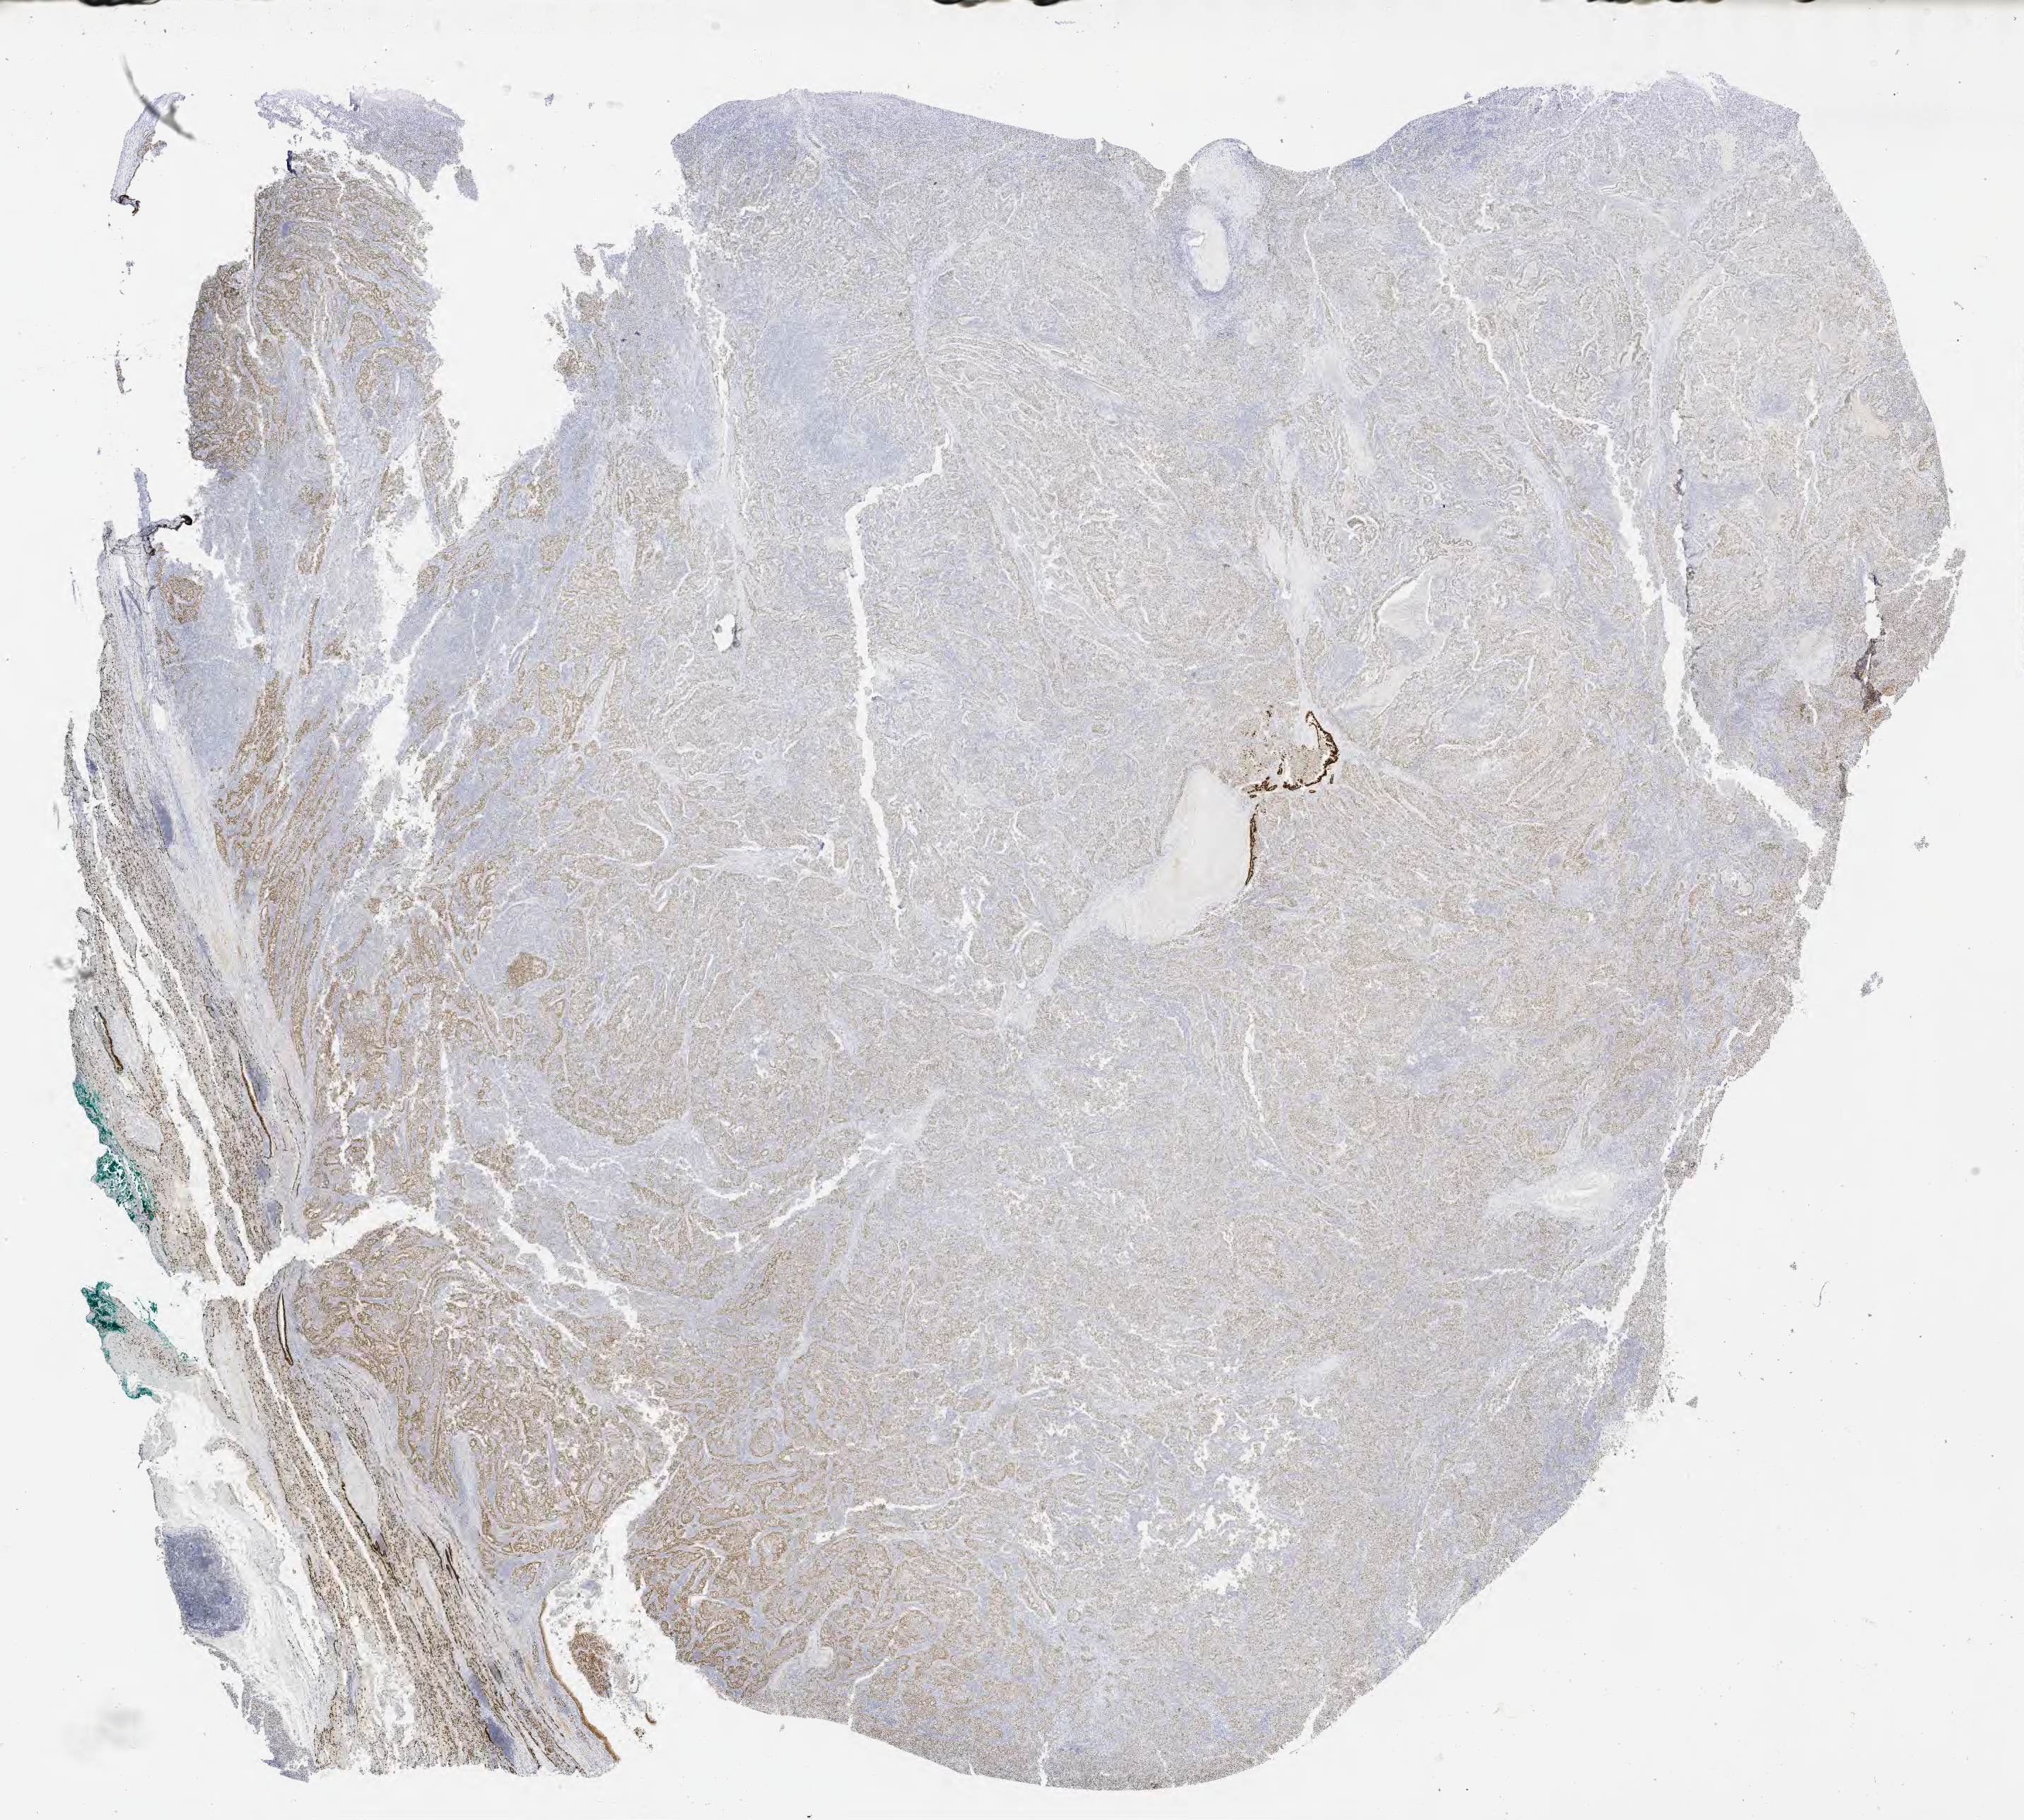
Whole-slide image, immunohistochemical stain for TTF-1 (thyroid transcription factor 1) — a low-resolution overview of the entire scanned area, about 23.1 x 20.8 mm. Specimen: tumor tissue. Site: lung (right). Patient: male, 52 years old.
Histologic diagnosis: Non-small cell carcinoma.